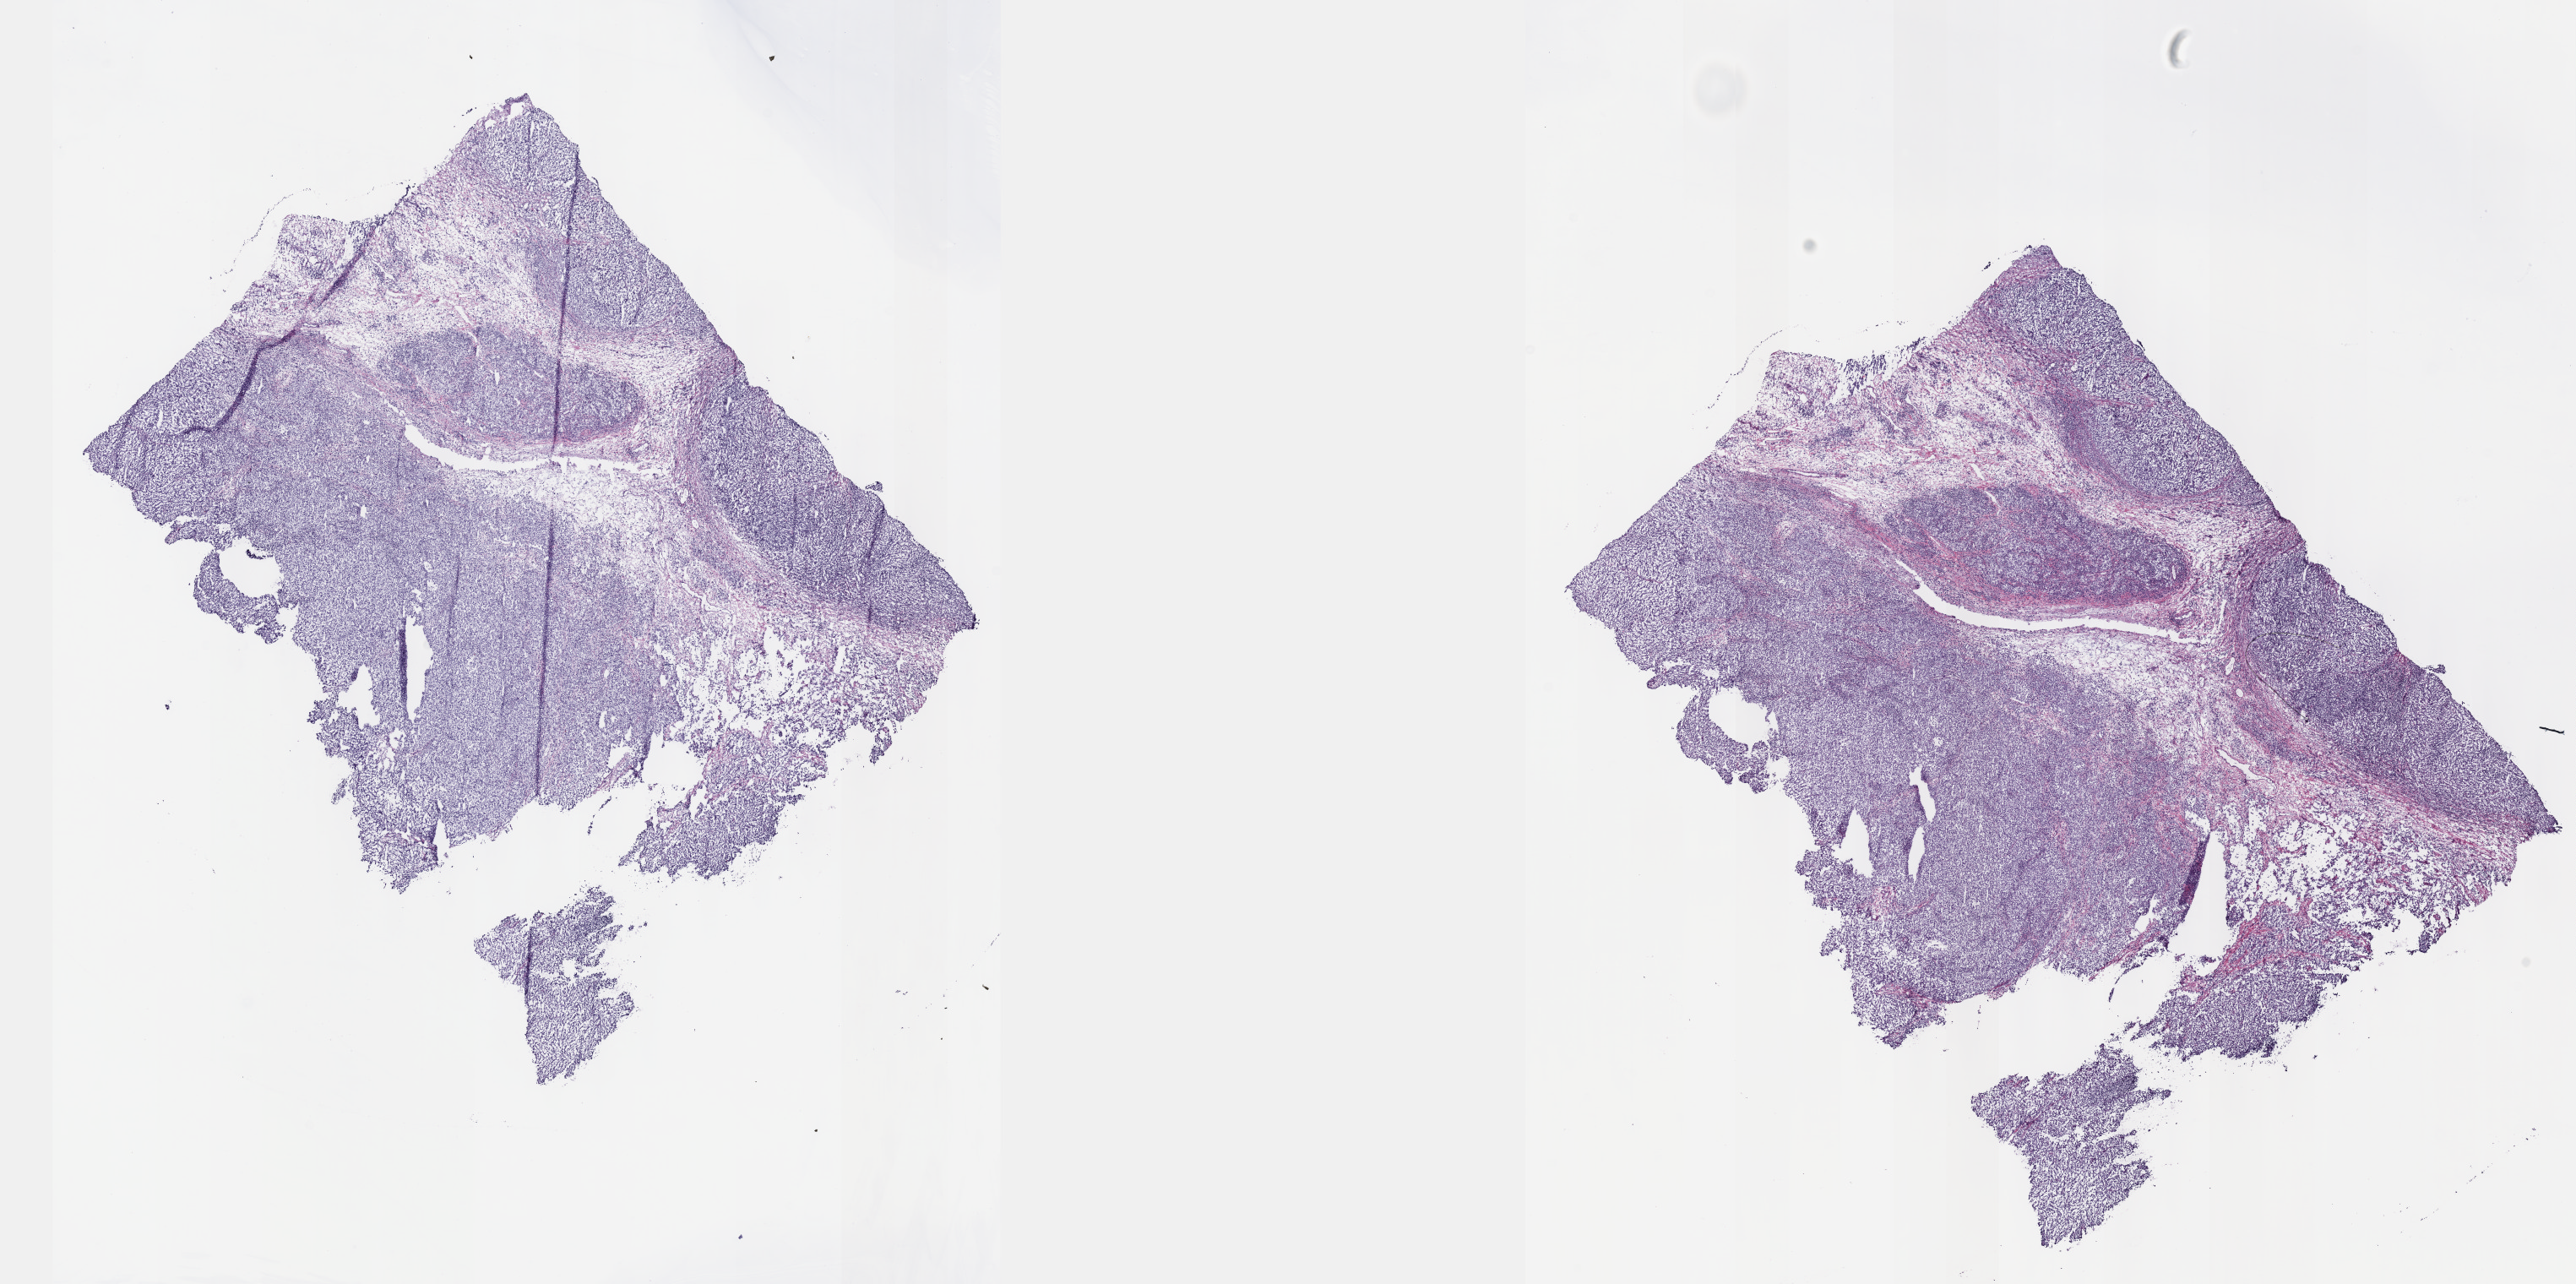
Hematoxylin and eosin (H&E) stained whole-slide image — low-resolution overview of the scanned area, about 24.6 x 12.3 mm. Frozen section. Testis, additional new primary tumour sample. Patient: male, age at initial diagnosis 22 years. Pathologist review of this section (percent, as recorded): tumour cells 90%, tumour nuclei 70%, normal cells 0%, stromal cells 10%, necrosis 0%. Infiltration values recorded for this section: lymphocyte infiltration 90%, monocyte infiltration 10%, neutrophil infiltration 0%.
- this section: additional new primary tumour
- patient diagnosis: Embryonal carcinoma, NOS